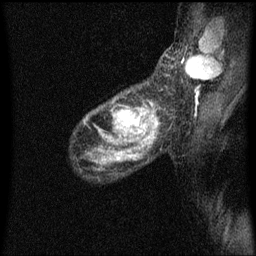
Breast MRI (dynamic contrast-enhanced), one sagittal slice; slice 44 of 60 in the series (ordered by position); dynamic contrast-enhanced series, image 2 of 3 at this slice position (ordered by acquisition); 1.5 T; TE 4.2 ms, TR 8.4 ms; 2 mm slice thickness; 256 × 256 image matrix, field of view 200 × 200 mm. Female patient, age 49 years.
Outlined on this slice (semi-automatic segmentation, software-assisted and operator-edited):
- analysis volume of interest (the breast-tissue region the enhancement analysis was run in; not a lesion): bounding box (x1, y1, x2, y2) in pixels: (103, 92, 157, 151)
- tumour enhancement mask (voxels above the 70 % enhancement threshold inside the analysis volume of interest): (120, 110, 144, 133)